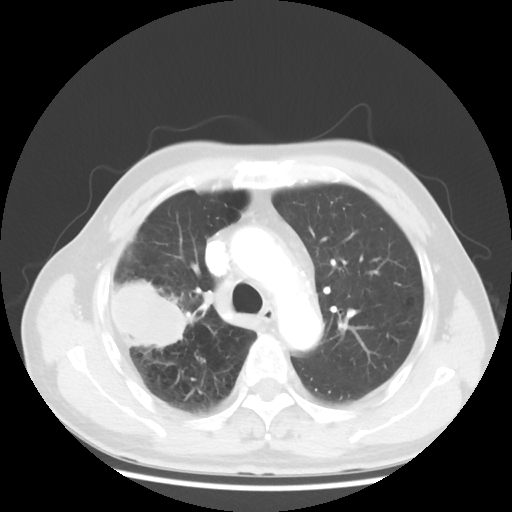
Chest CT, one axial slice. Position 35 of 50 along the scan axis. Reconstruction kernel STANDARD. 120 kVp. Lung window (W 1500 / L -600 HU). 5 mm slice thickness. 512 × 512 image matrix, field of view 360 × 360 mm. Patient: male, 69 years. From the clinical record (not read from this slice): clinical TNM (as recorded): T3 N0 M0; histopathological grade: G3.
Outlined on this slice (rectangle marked by the reading radiologist):
- lung tumour (recorded histology: adenocarcinoma): bounding box (x1, y1, x2, y2) in pixels: (109, 273, 192, 350)